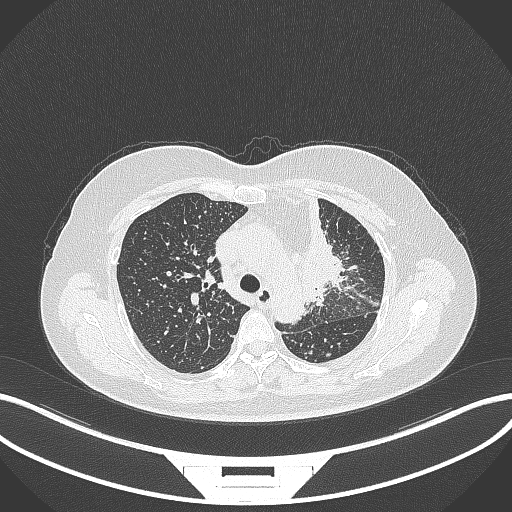
Chest CT, one axial slice; slice 236 of 348 in the series (ordered by position); reconstruction kernel B70f; 120 kVp; lung window (W 1500 / L -600 HU); 512 × 512 image matrix, field of view 400 × 400 mm. Patient: female, 49 years. From the clinical record (not read from this slice): clinical TNM (as recorded): T1c N0 M1.
Structures marked on this image (bounding box drawn by a radiologist):
- lung tumour (recorded histology: adenocarcinoma): box from (x=290, y=199) to (x=348, y=313) px